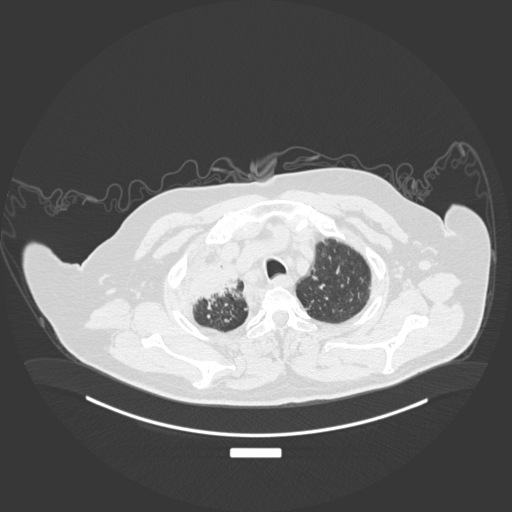
Chest CT, one axial slice; slice 165 of 201 in the series (ordered by position); reconstruction kernel B30f; 120 kVp; lung window (W 1500 / L -600 HU); 1 mm slice thickness; 512 × 512 image matrix, field of view 500 × 500 mm. Male patient, age 69 years. From the clinical record (not read from this slice): clinical TNM (as recorded): T4 N3 M1.
Outlined on this slice (bounding box drawn by a radiologist):
- lung tumour (recorded histology: adenocarcinoma): bounding box [x1, y1, x2, y2] px = [188, 253, 244, 307]